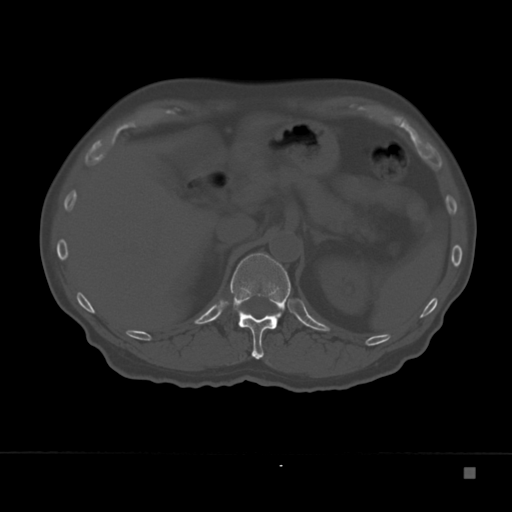
CT including the spine, one axial slice; position 129 of 332 along the scan axis; 120 kVp; bone window (W 1800 / L 400 HU); 1.5 mm slice thickness; 512 × 512 image matrix, field of view 389 × 389 mm. Patient: male, 72 years. From the clinical record (not read from this slice): primary cancer: skeletal.
Structures marked on this image (semi-automatically segmented with operator editing):
- T12 vertebra: box from (x=230, y=253) to (x=291, y=359) px